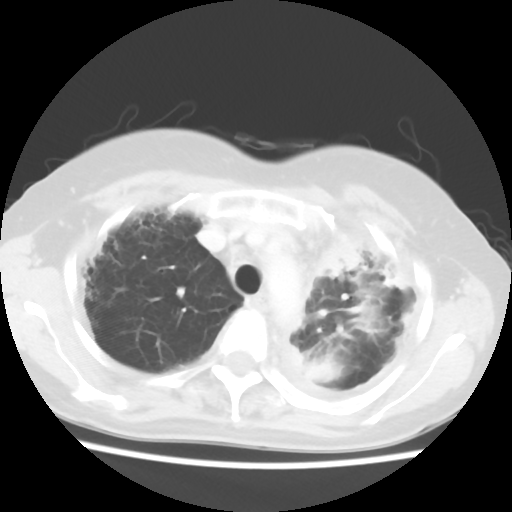
Chest CT, one axial slice; lung window (W 1500 / L -600 HU); 5 mm slice thickness; 512 × 512 image matrix, field of view 309 × 309 mm. Female patient, age 56 years. Case-level facts recorded for this patient, not image findings: clinical TNM (as recorded): T1c N0 M1.
Annotated regions visible in this slice (bounding box drawn by a radiologist):
- lung tumour (recorded histology: adenocarcinoma): box from (x=321, y=233) to (x=360, y=289) px